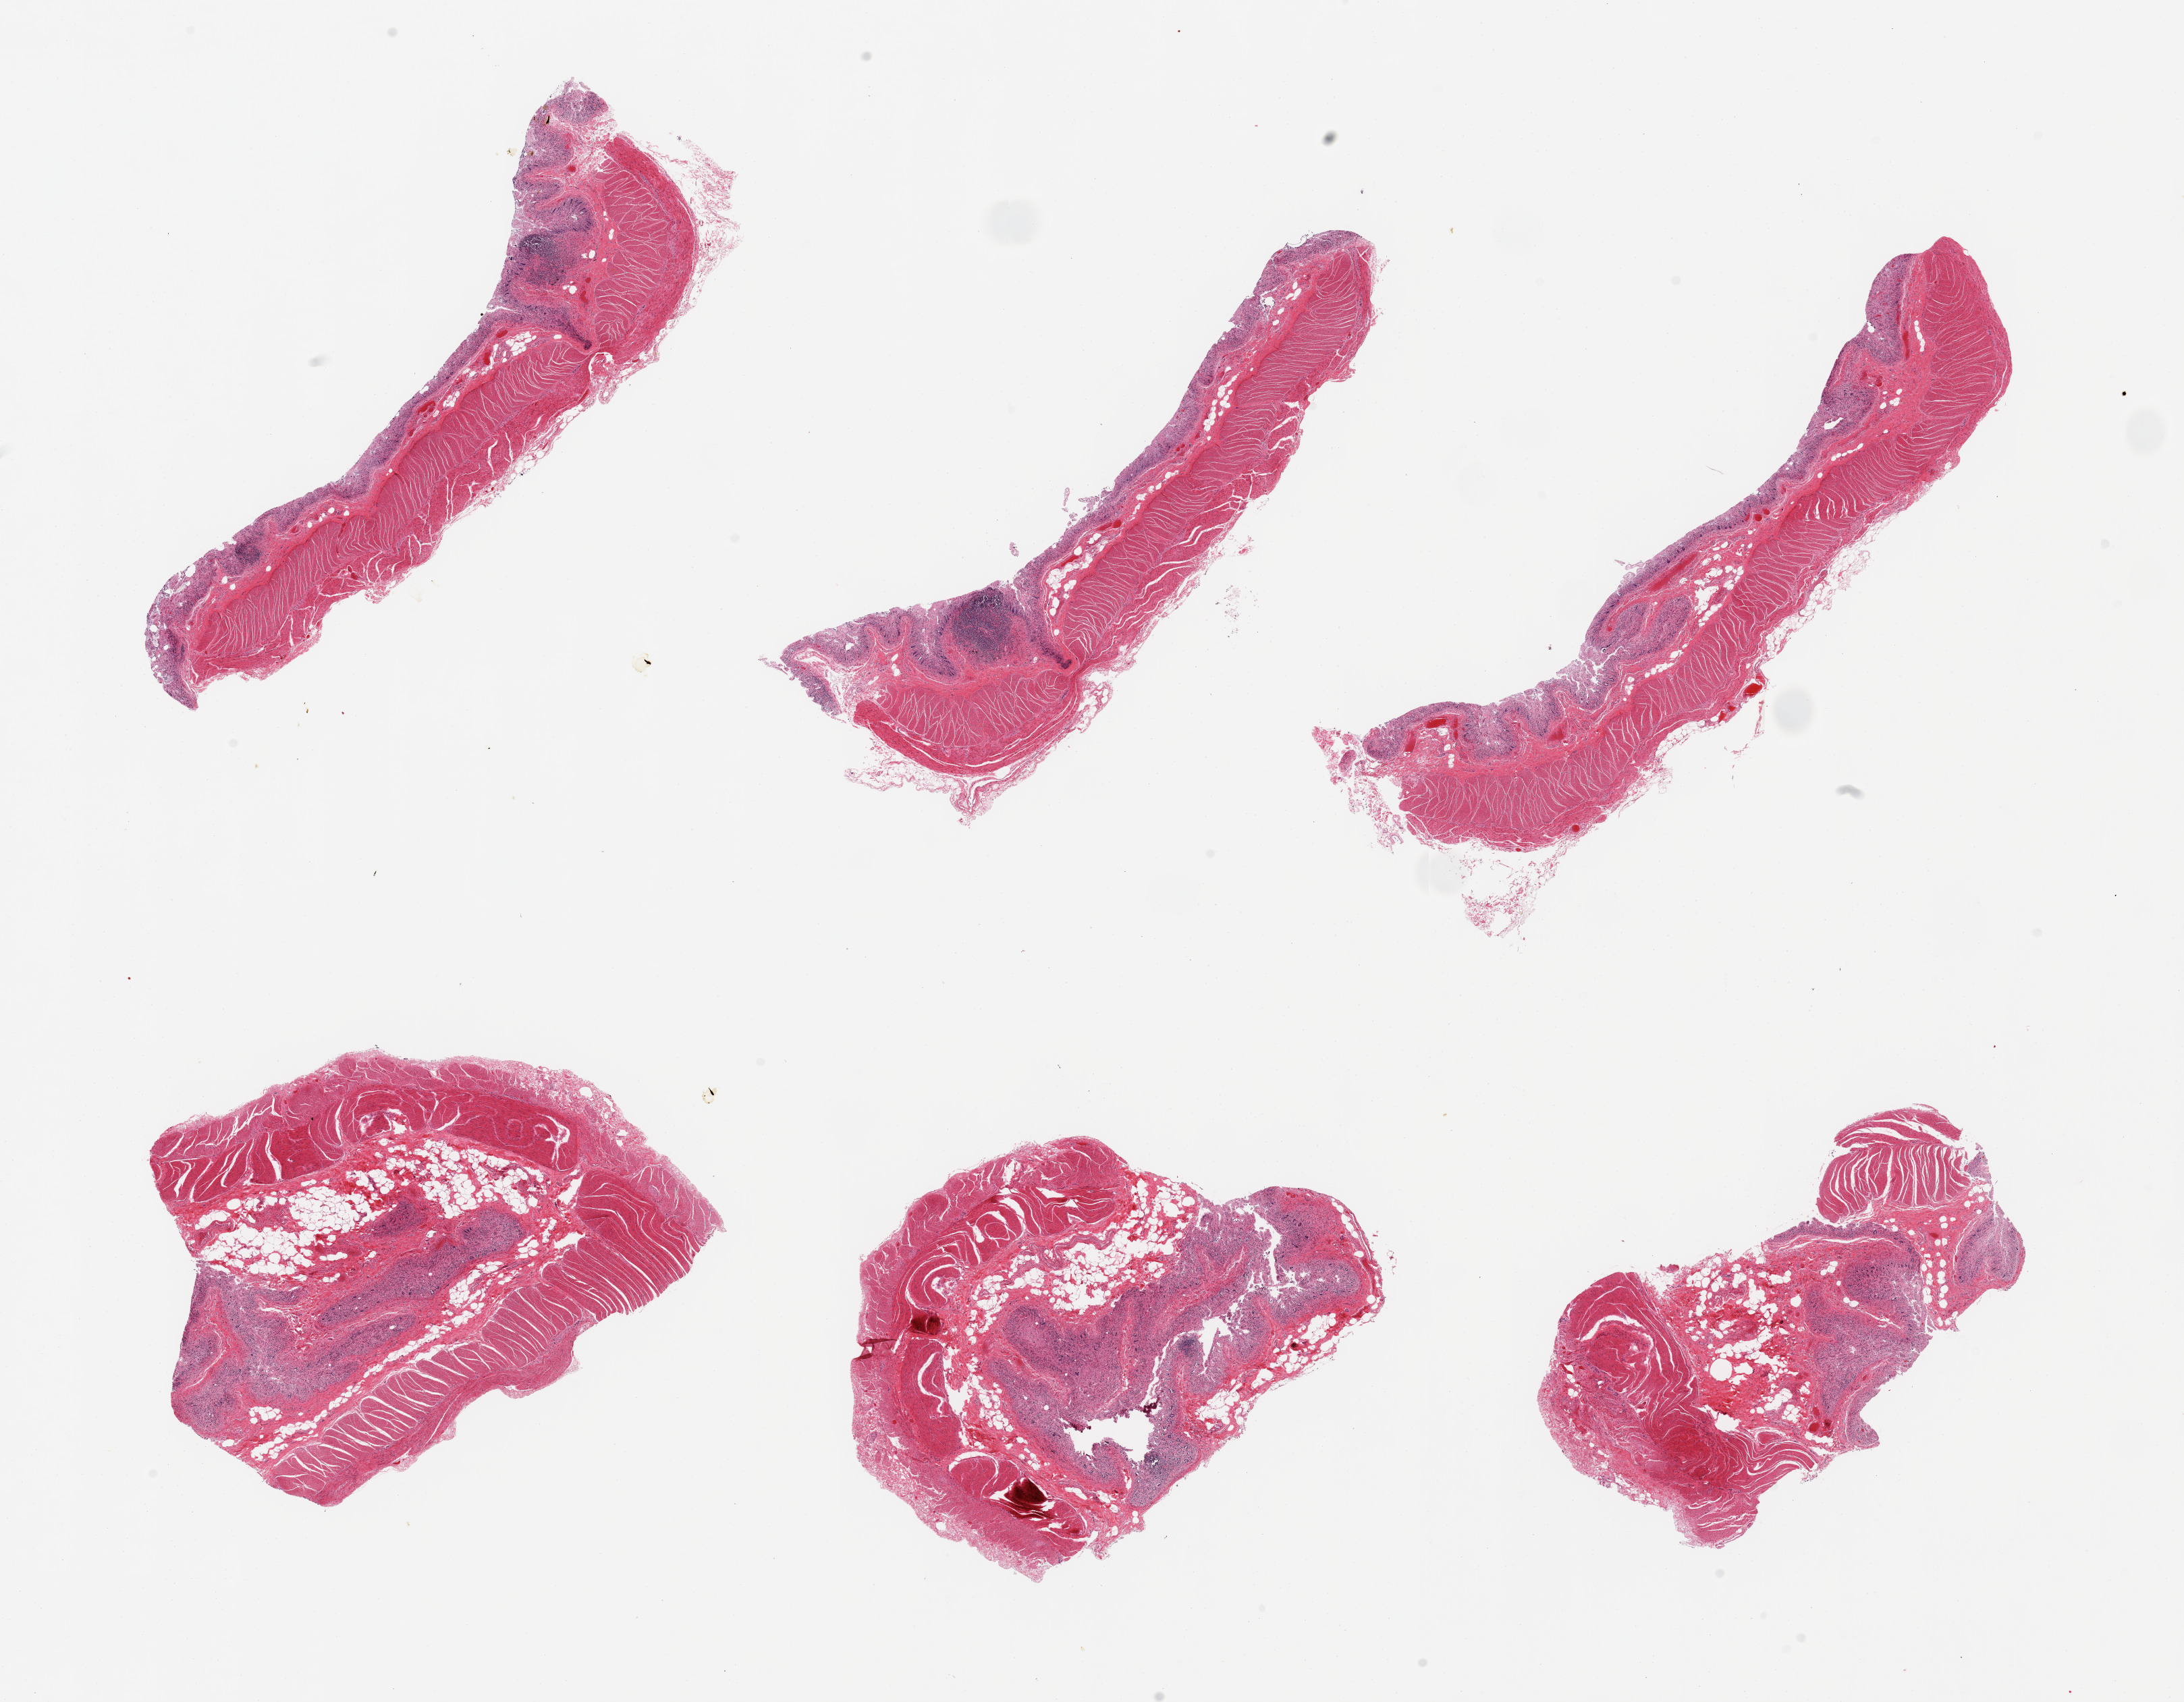
Whole-slide image, haematoxylin and eosin stain, brightfield — a low-resolution overview of the entire scanned area, about 25.6 x 19.9 mm. Male donor.
Specimen: PAXgene-fixed, paraffin-embedded tissue; target tissue: ileum; tissue donor sample.